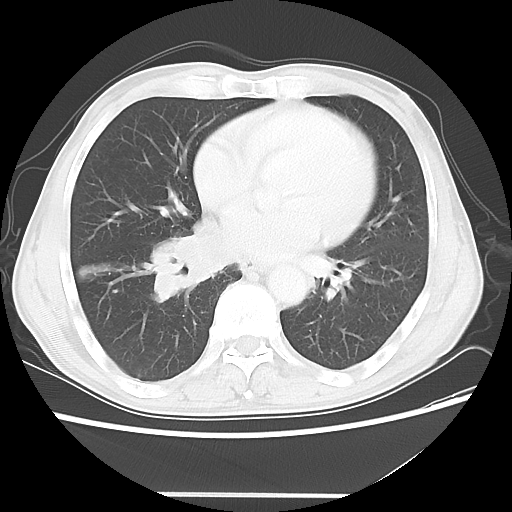
Chest CT, one axial slice. Position 23 of 56 along the scan axis. Reconstruction kernel LUNG. Lung window (W 1500 / L -600 HU). 5 mm slice thickness. 512 × 512 image matrix, field of view 344 × 344 mm. Patient: male, 65 years. From the clinical record (not read from this slice): clinical TNM (as recorded): T1c N3 M0; histopathological grade: G3.
Annotated regions visible in this slice (rectangle marked by the reading radiologist):
- lung tumour (recorded histology: small cell carcinoma): bounding box <145,223,260,307> (left, top, right, bottom; pixels)